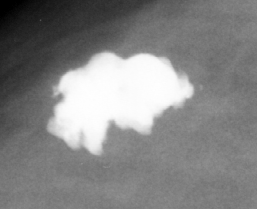
Region of interest cut from a scanned film mammogram (one marked finding); right breast; CC view; BI-RADS breast density category 4 (scale 1–4).
Calcifications, morphology coarse; BI-RADS assessment category 2; subtlety rating 5 on a 1 (subtle) to 5 (obvious) scale; benign without callback (not worked up further).